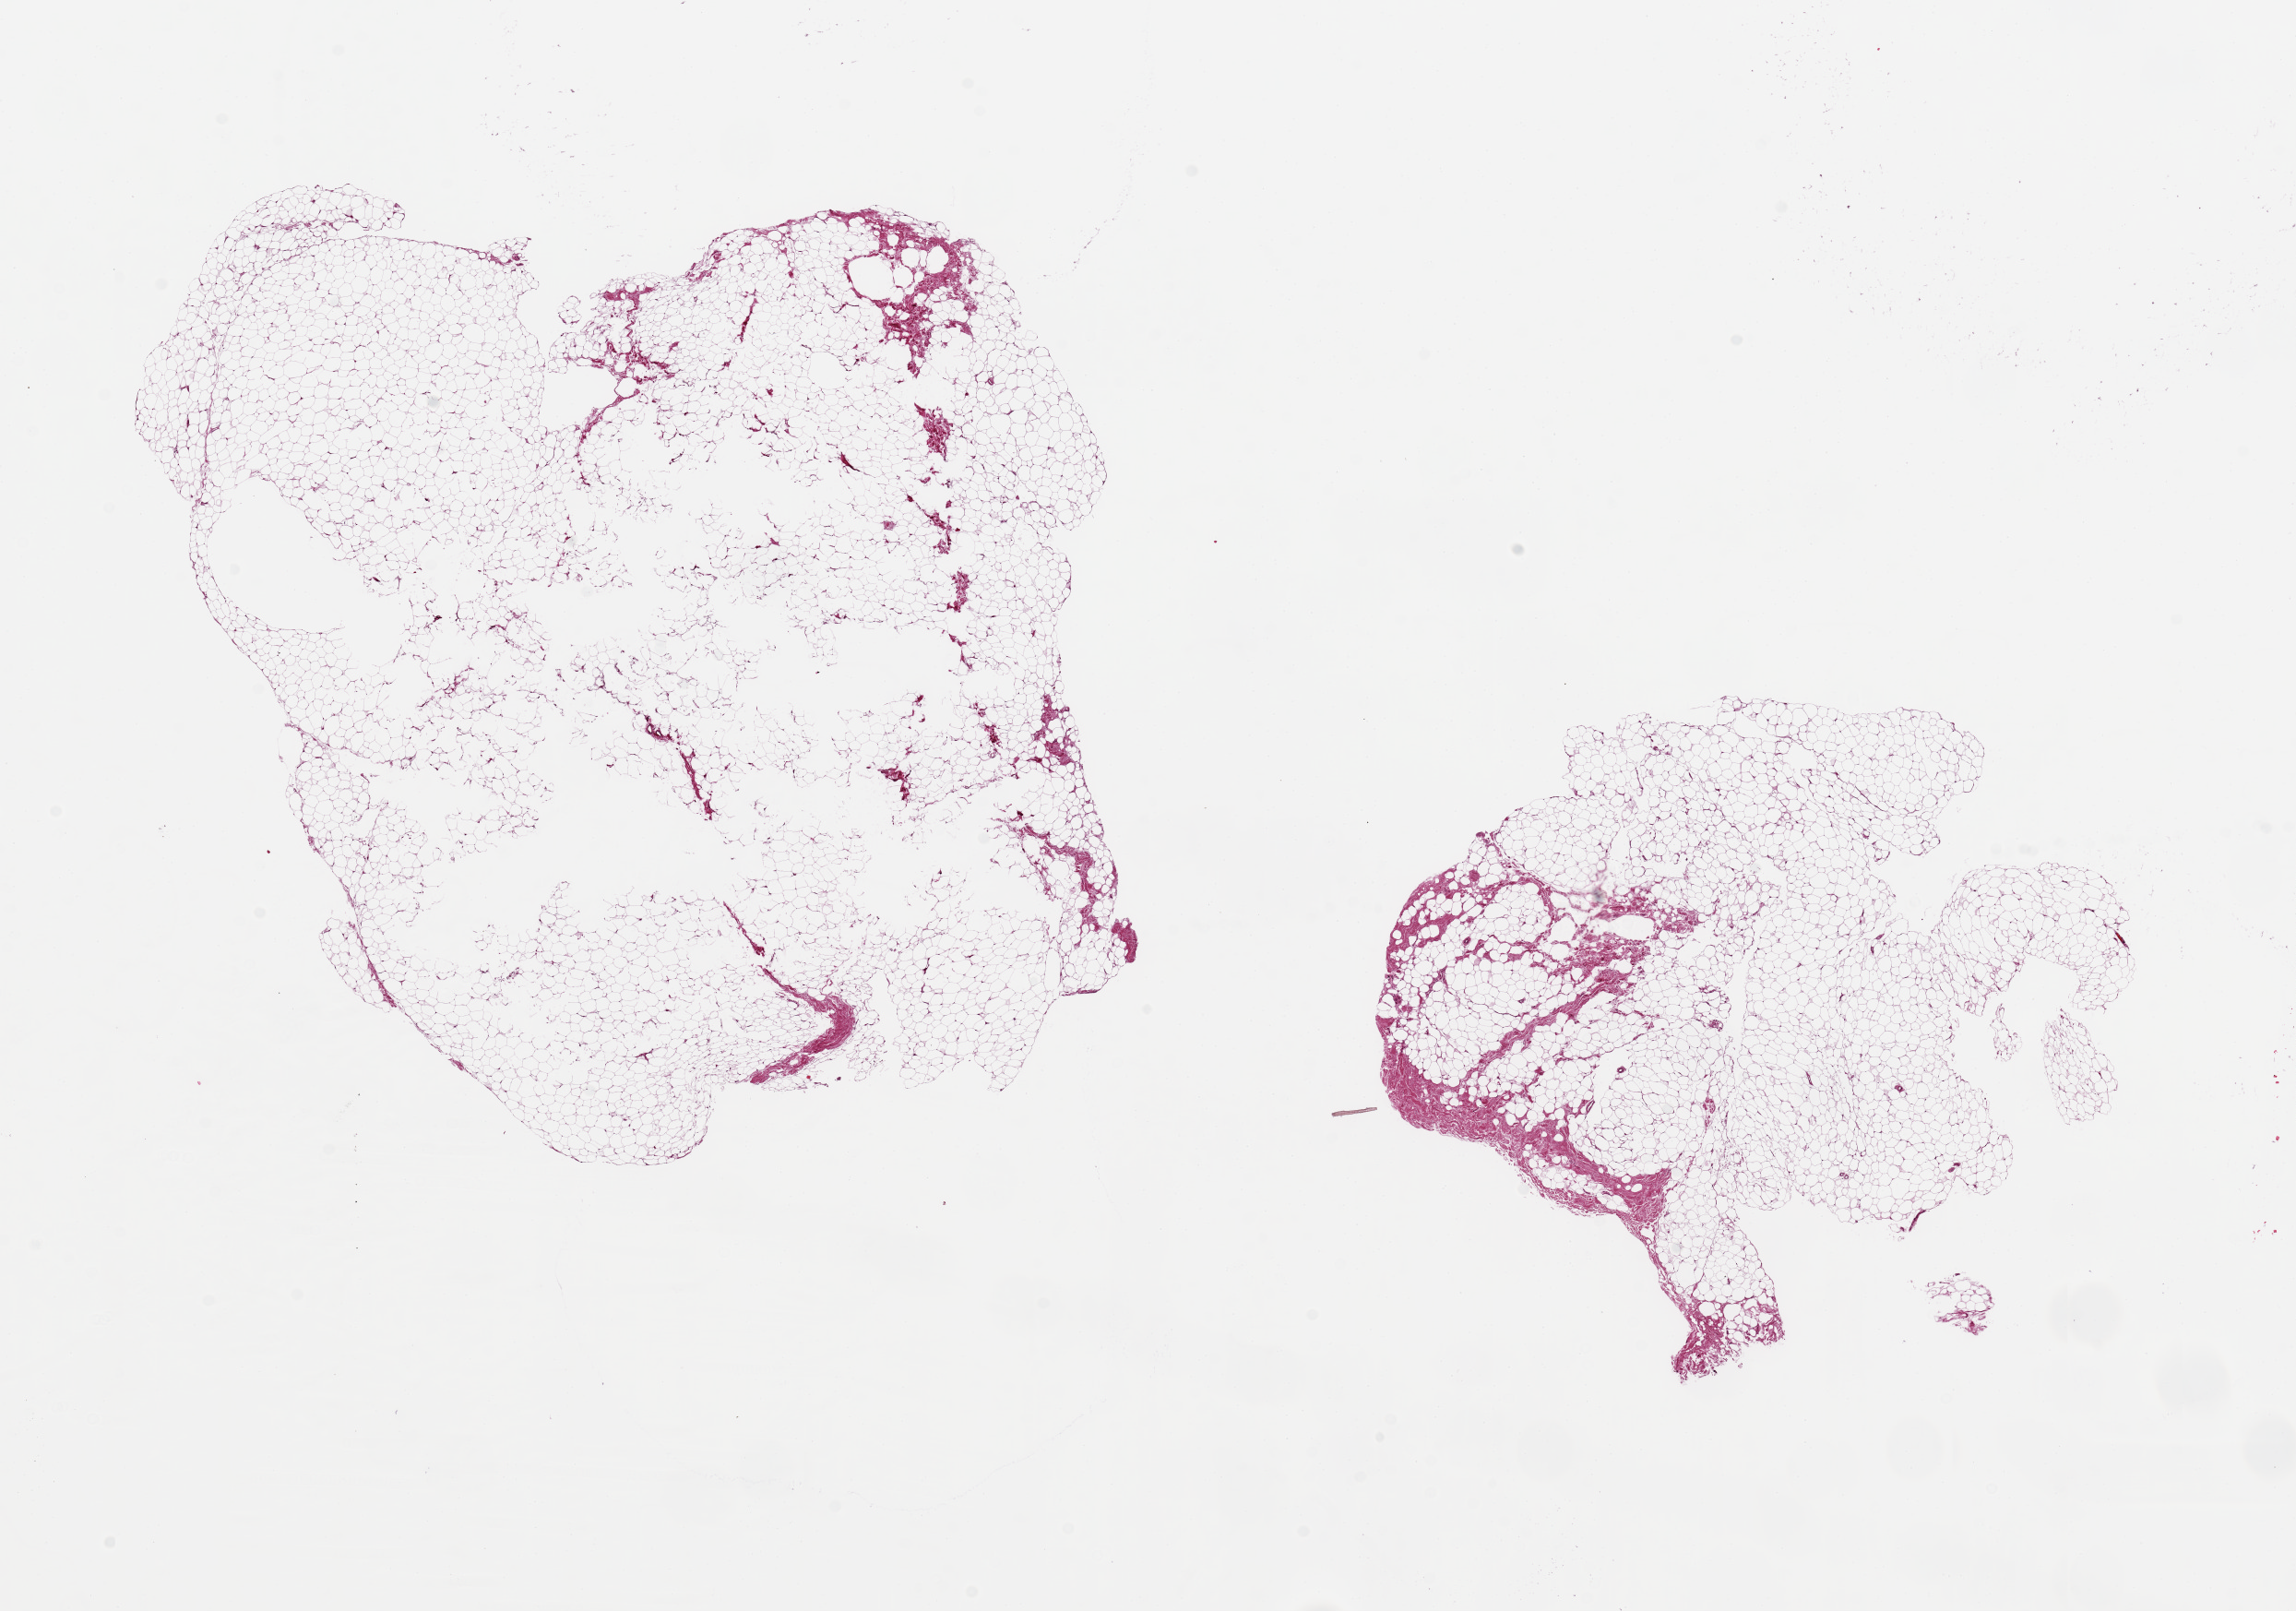
Hematoxylin and eosin (H&E) whole-slide image, brightfield, low-resolution overview of the scanned area, about 19.7 x 13.8 mm; PAXgene-fixed paraffin-embedded (PFPE) section; target tissue: breast; tissue donor sample. Donor sex: male.
Pathologist's review note for this sample: 2 aliquots ~7x7mm. All adipose tissue, no ductal elements noted.